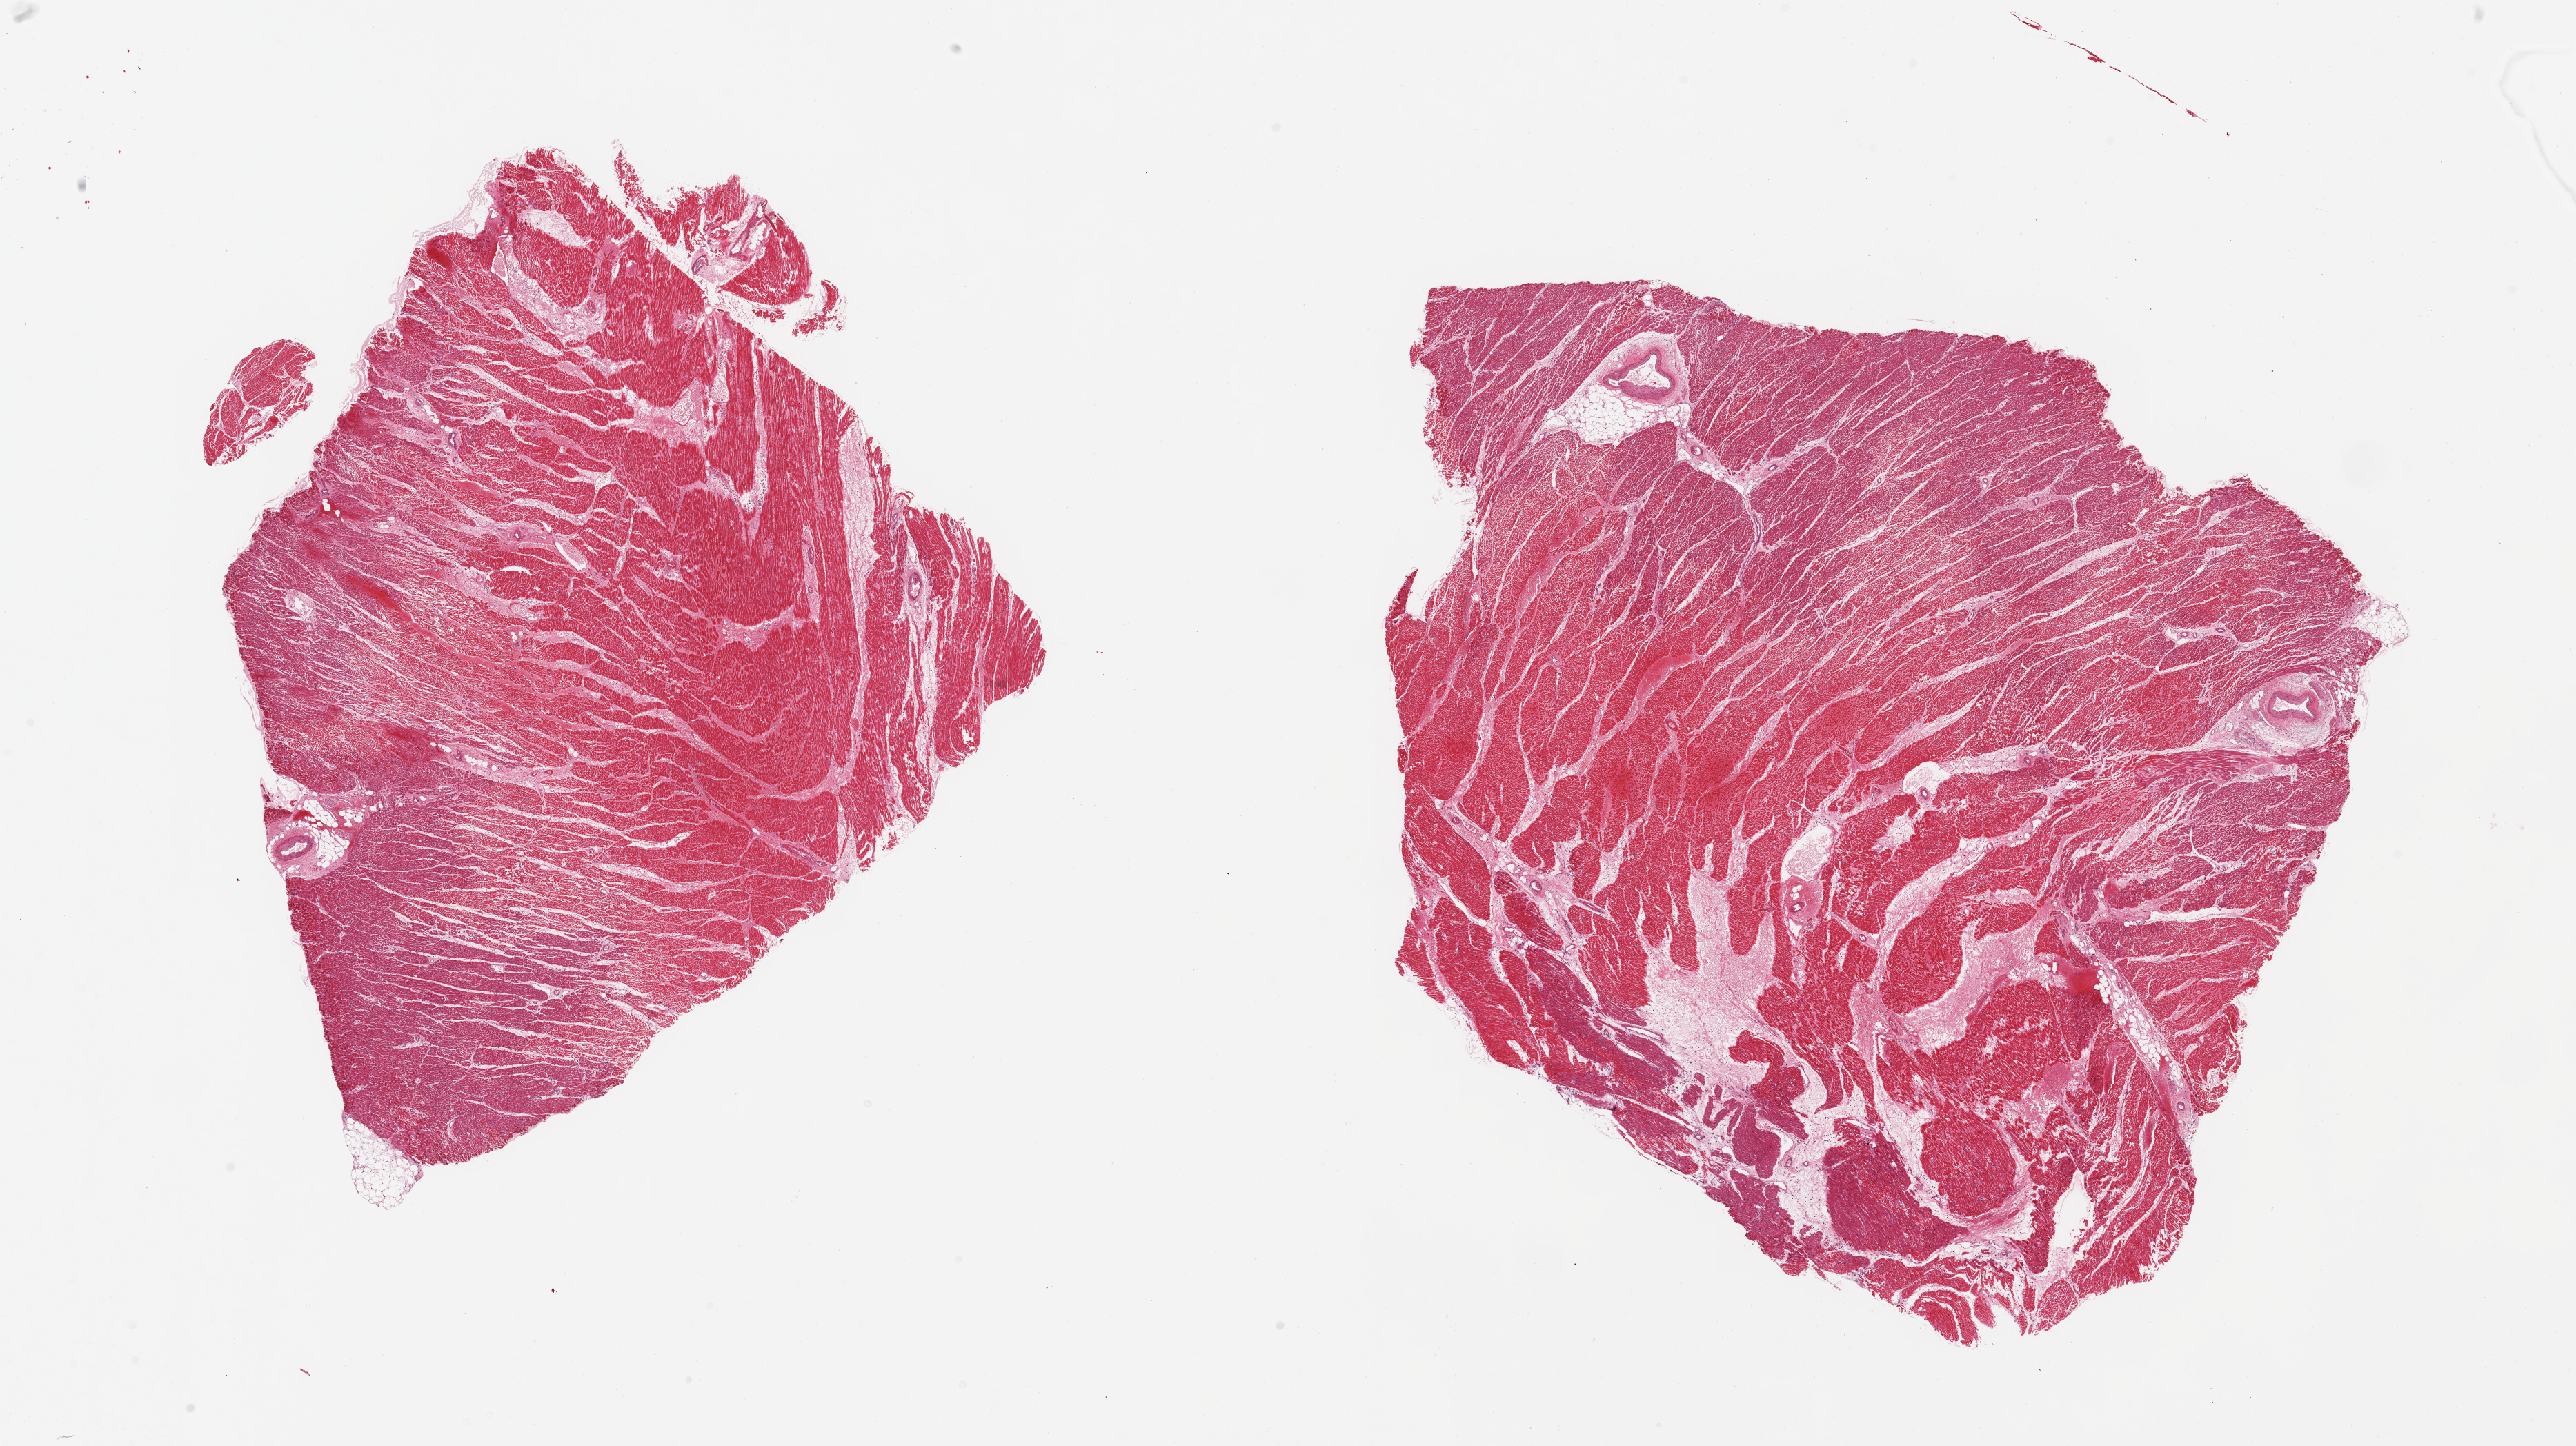
Whole-slide image, hematoxylin and eosin (H&E) stain, a low-resolution overview of the entire scanned area, about 29.5 x 16.6 mm; PAXgene-fixed paraffin-embedded (PFPE) section; target tissue: heart; tissue donor sample. Donor: female.
• pathologist's review note for this sample: 2 pieces, subacute myocardial infarct, (~24-48 hours old), ~1 cm